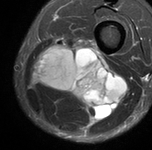
MRI of an extremity soft-tissue mass, one axial slice; slice 34 of 90 in the series (ordered by position); STIR; MR volume resampled by the dataset authors to the PET/CT grid (not the native acquisition matrix); 152 × 150 image matrix, field of view 148 × 146 mm. Male patient. From the clinical record (not read from this slice): histological type: undifferentiated pleomorphic liposarcoma; grade: high; site of the primary tumour: left thigh.
Structures marked on this image (expert contour drawn on MRI and transferred to this co-registered scan by the dataset authors):
- gross tumour volume including surrounding oedema: bounding box (x1, y1, x2, y2) in pixels: (32, 39, 124, 122)
- gross tumour volume (mass): (41, 53, 117, 111)